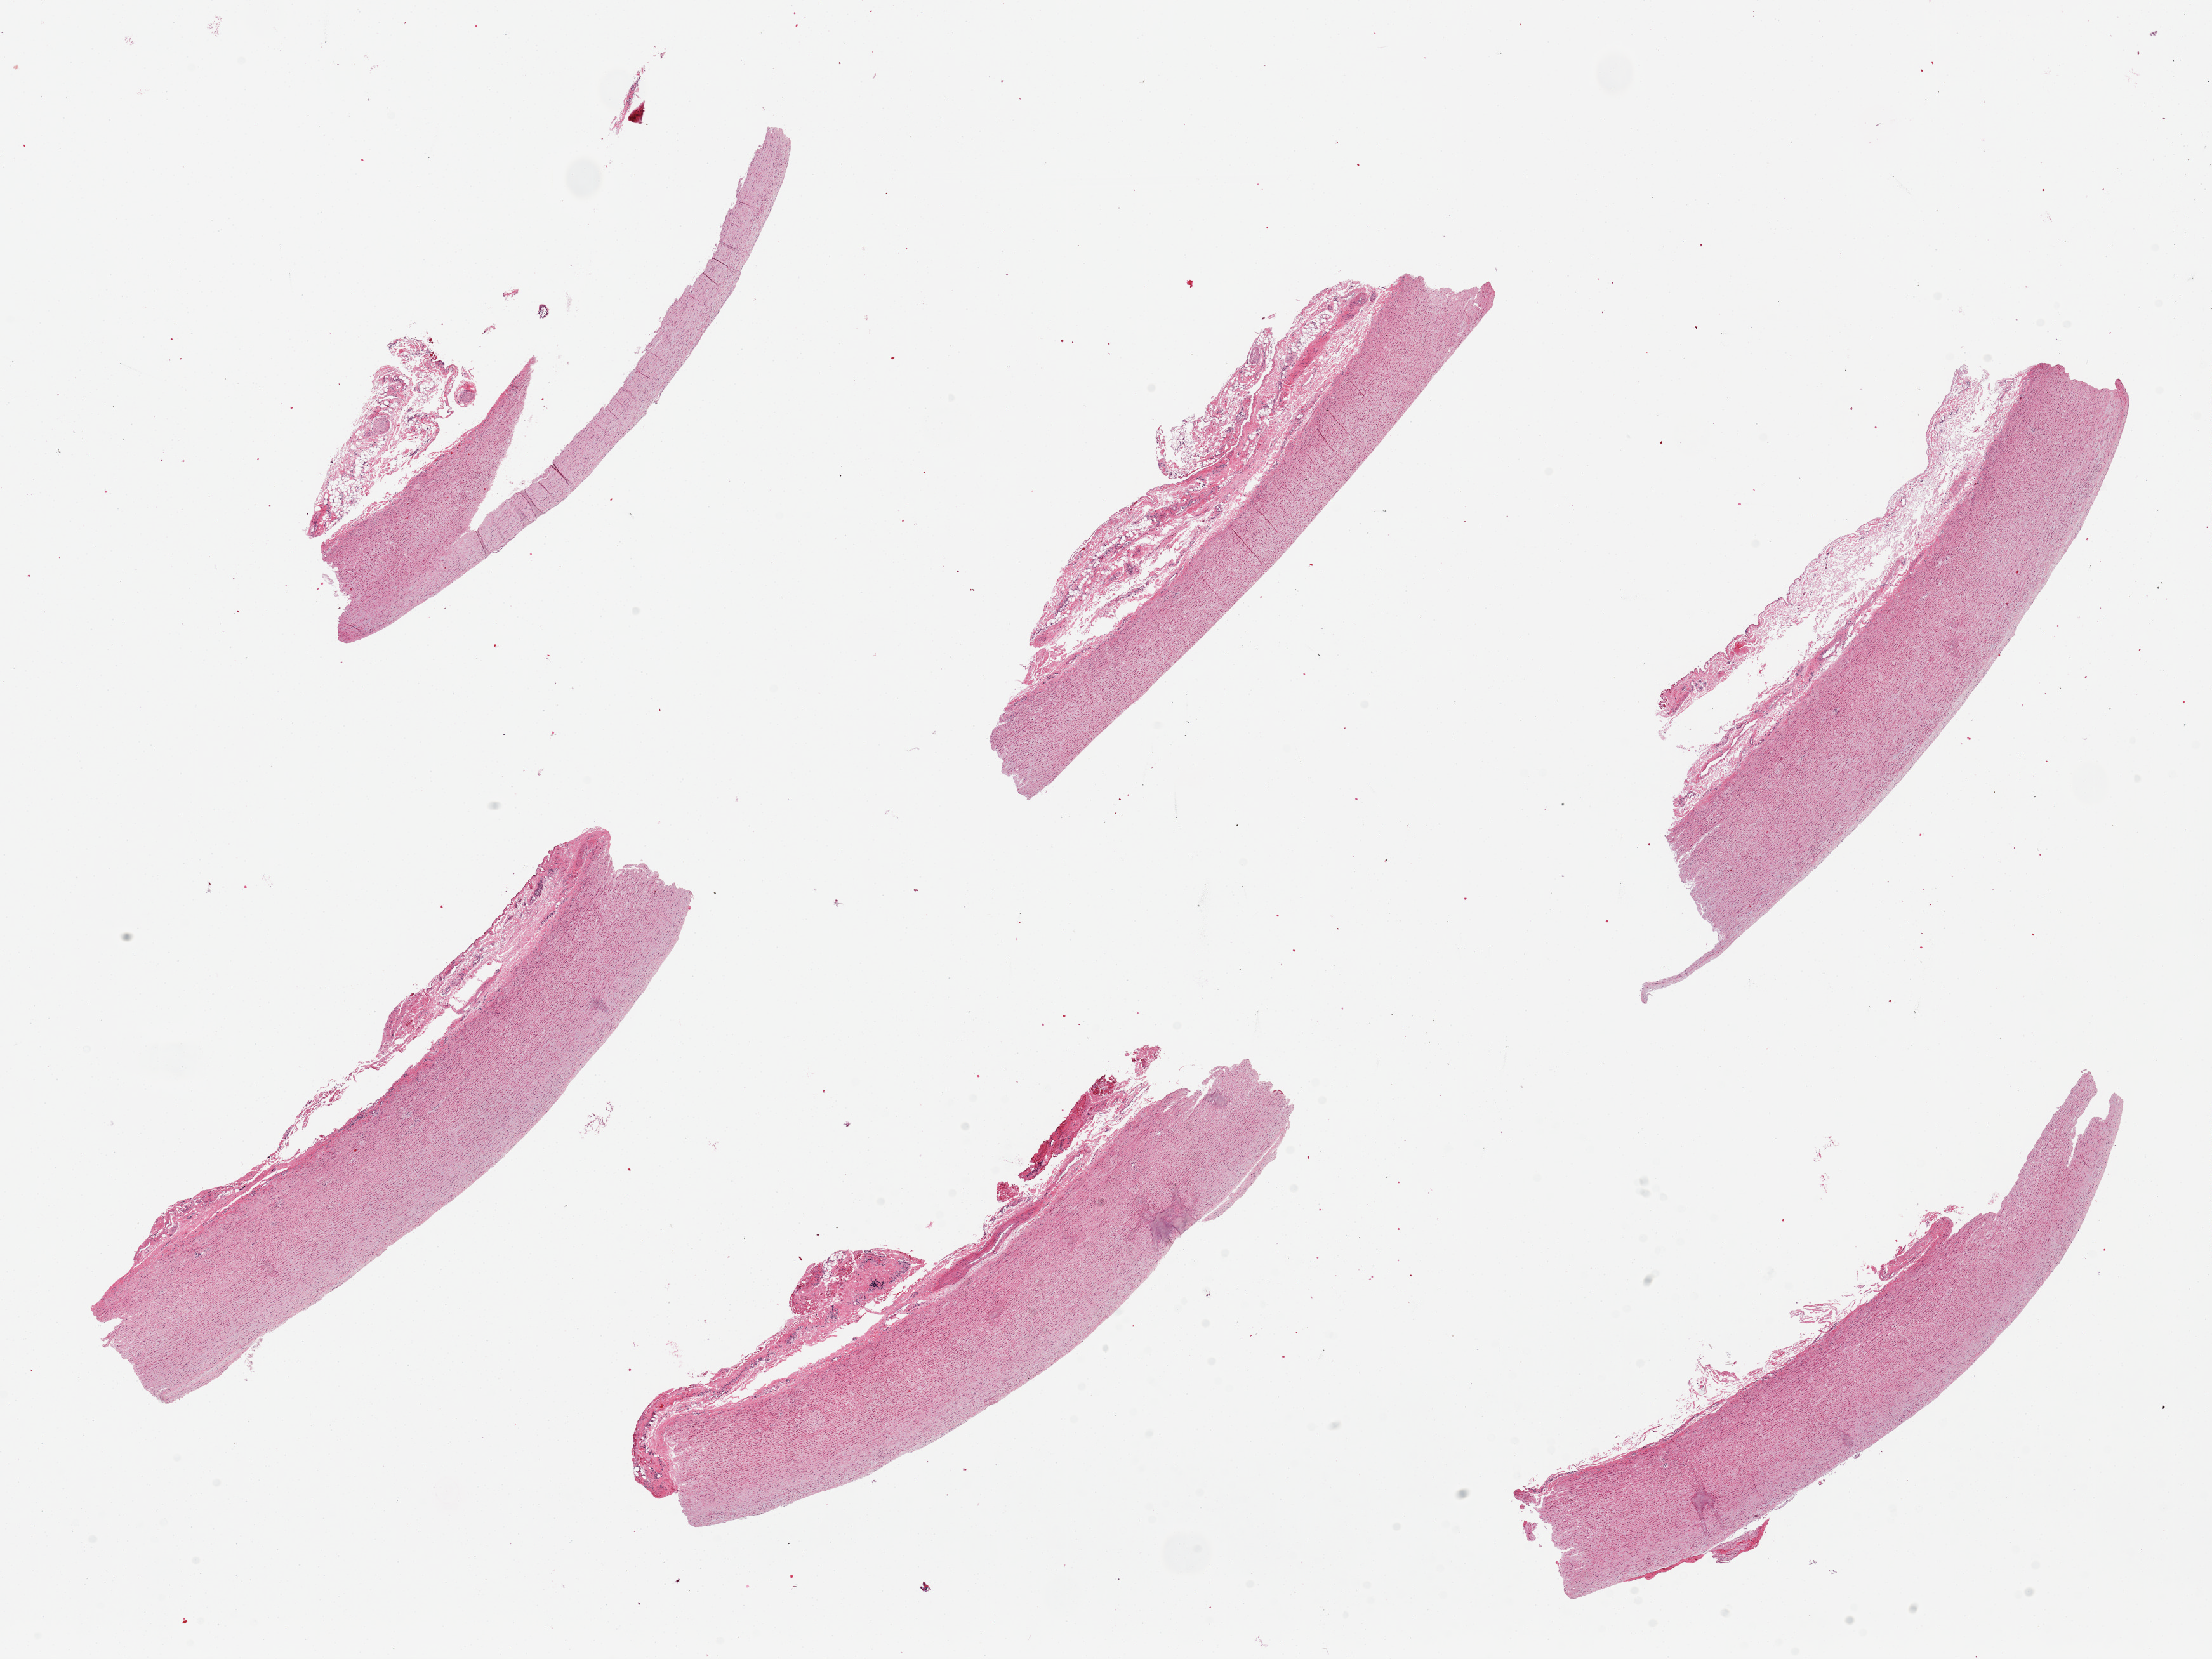
Hematoxylin and eosin (H&E) whole-slide image, brightfield — shown as a low-resolution overview of the whole scanned area (about 27.6 x 20.7 mm). PAXgene-fixed, paraffin-embedded tissue. Sampled site (target tissue): aorta. Tissue donor sample. Female donor.
* reviewer comment on this tissue sample: 6 pieces. up to 8x3mm; Fibrofatty adventitia on all up to 1 mm thick. No plaques